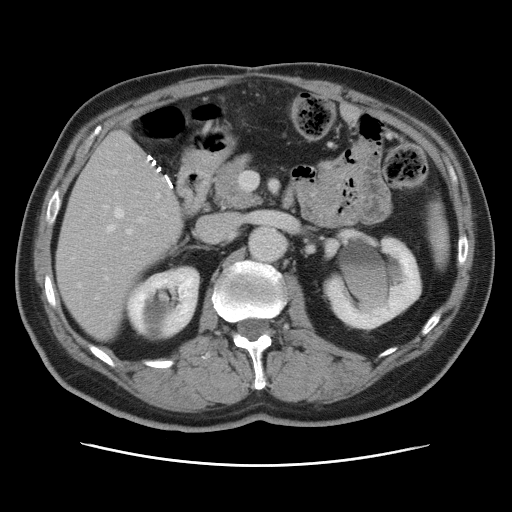
Contrast-enhanced abdominal CT, one axial slice; position 37 of 80 along the scan axis; soft-tissue window (W 400 / L 40 HU); 5 mm slice thickness; 512 × 512 image matrix, field of view 370 × 370 mm. Male patient, age 69 years. Case-level facts recorded for this patient, not image findings: diagnosis: colorectal cancer liver metastases, imaged before liver resection; multiple liver metastases: no; largest metastasis: 5 cm; disease in both lobes: yes.
Structures marked on this image (manually delineated by an expert):
- hepatic veins: box from (x=78, y=208) to (x=142, y=287) px
- liver: (x=57, y=129)–(x=183, y=339)
- planned liver remnant (the part of the liver to remain after resection): (x=57, y=193)–(x=184, y=339)
- portal vein (with intrahepatic branches): (x=105, y=171)–(x=133, y=280)